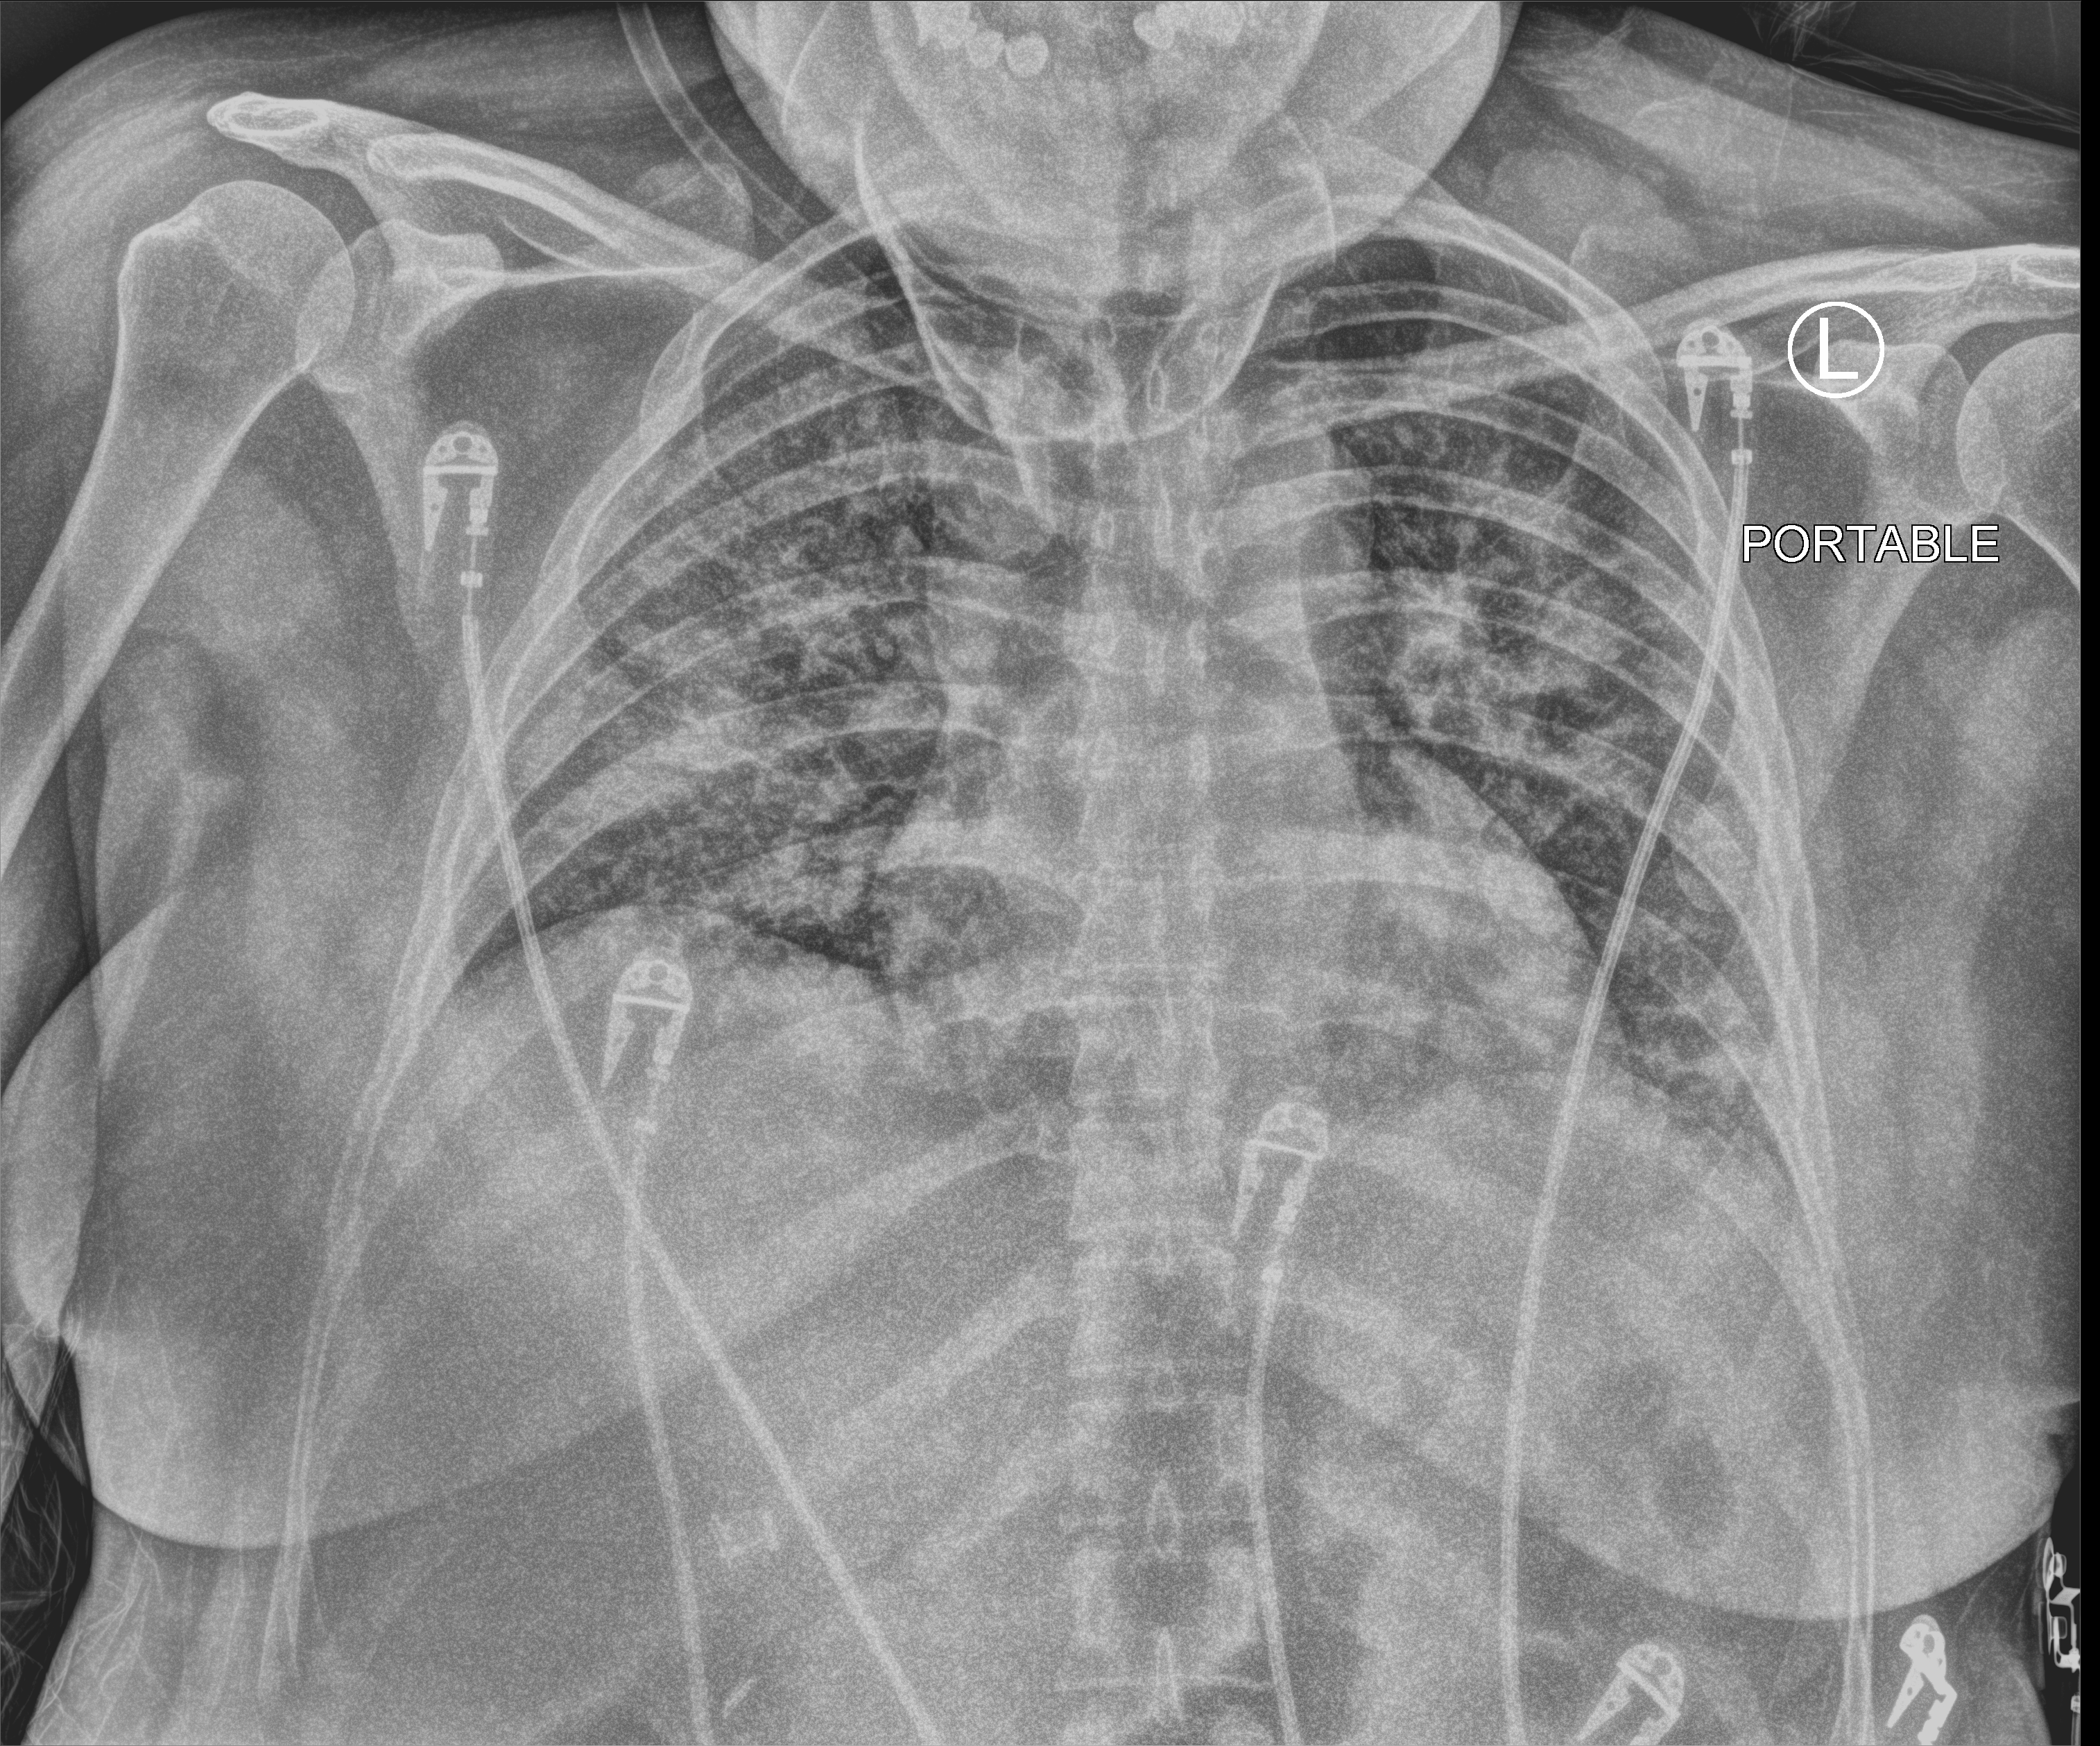
Chest X-ray (portable), anteroposterior (AP) projection. Patient hospitalised with COVID-19; female, aged 18–59 years.
Admission-level facts for this patient (not findings on this image; timing relative to this image not recorded):
- chronic kidney disease (admission record): no